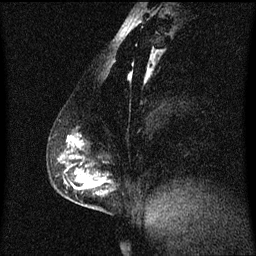
Breast MRI (dynamic contrast-enhanced), one sagittal slice; position 27 of 60 along the scan axis; dynamic contrast-enhanced series, image 2 of 3 at this slice position (ordered by acquisition); 1.5 T; TE 4.2 ms, TR 8.4 ms; 2 mm slice thickness; 256 × 256 image matrix, field of view 200 × 200 mm. Patient: female, 40 years. Case-level facts recorded for this patient, not image findings: setting: breast cancer imaged before/during neoadjuvant chemotherapy; receptor status: triple-negative.
Outlined on this slice (semi-automatically segmented with operator editing):
- analysis volume of interest (the breast-tissue region the enhancement analysis was run in; not a lesion): bounding box [x1, y1, x2, y2] px = [58, 134, 113, 211]
- tumour enhancement mask (voxels above the 70 % enhancement threshold inside the analysis volume of interest): [66, 138, 109, 195]